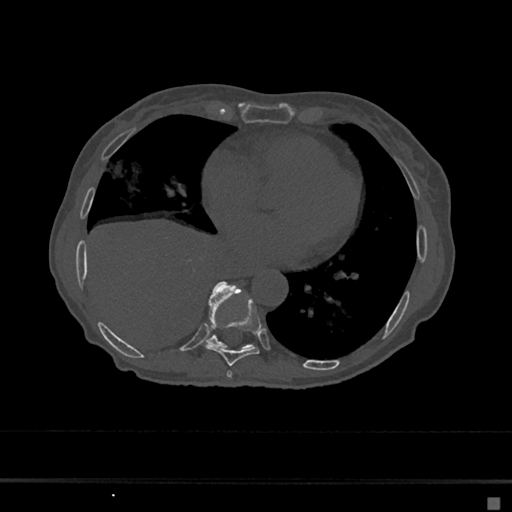
CT including the spine, one axial slice. Position 307 of 797 along the scan axis. Reconstruction kernel Br40s/3. 120 kVp. Bone window (W 1800 / L 400 HU). 0.5 mm slice thickness. 512 × 512 image matrix, field of view 360 × 360 mm. Patient: female, 68 years. From the clinical record (not read from this slice): primary cancer: renal.
Structures marked on this image (semi-automatically segmented with operator editing):
- T7 vertebra: box from (x=226, y=371) to (x=232, y=379) px
- T8 vertebra: (x=205, y=297)–(x=261, y=366)
- T9 vertebra: (x=208, y=281)–(x=253, y=349)